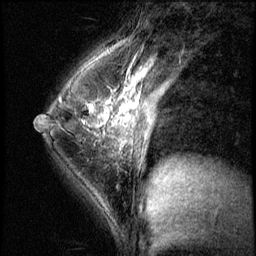
Breast MRI (dynamic contrast-enhanced), one sagittal slice. Position 38 of 56 along the scan axis. 3 images stored at this slice position (order not interpretable as contrast timing). 1.5 T. TE 4.2 ms, TR 8.7 ms. 2.5 mm slice thickness. 256 × 256 image matrix. Patient: female, 35 years. Case-level facts recorded for this patient, not image findings: setting: breast cancer imaged before/during neoadjuvant chemotherapy; receptor status: HER2-positive.
Annotated regions visible in this slice (semi-automatic segmentation, software-assisted and operator-edited):
- analysis volume of interest (the breast-tissue region the enhancement analysis was run in; not a lesion): bounding box (x1, y1, x2, y2) in pixels: (58, 84, 138, 186)
- tumour enhancement mask (voxels above the 140 % enhancement threshold inside the analysis volume of interest): (60, 98, 98, 126)